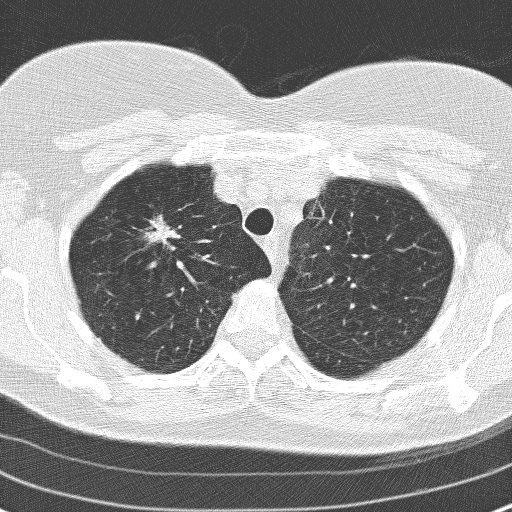
Low-dose screening chest CT, one axial slice; 120 kVp; lung window (W 1500 / L -600 HU); 3.2 mm slice thickness; 512 × 512 image matrix, field of view 313 × 313 mm.
Structures marked on this image (expert manual segmentation):
- lesion 1 (tumor, upper lobe of right lung): box from (x=149, y=223) to (x=172, y=242) px